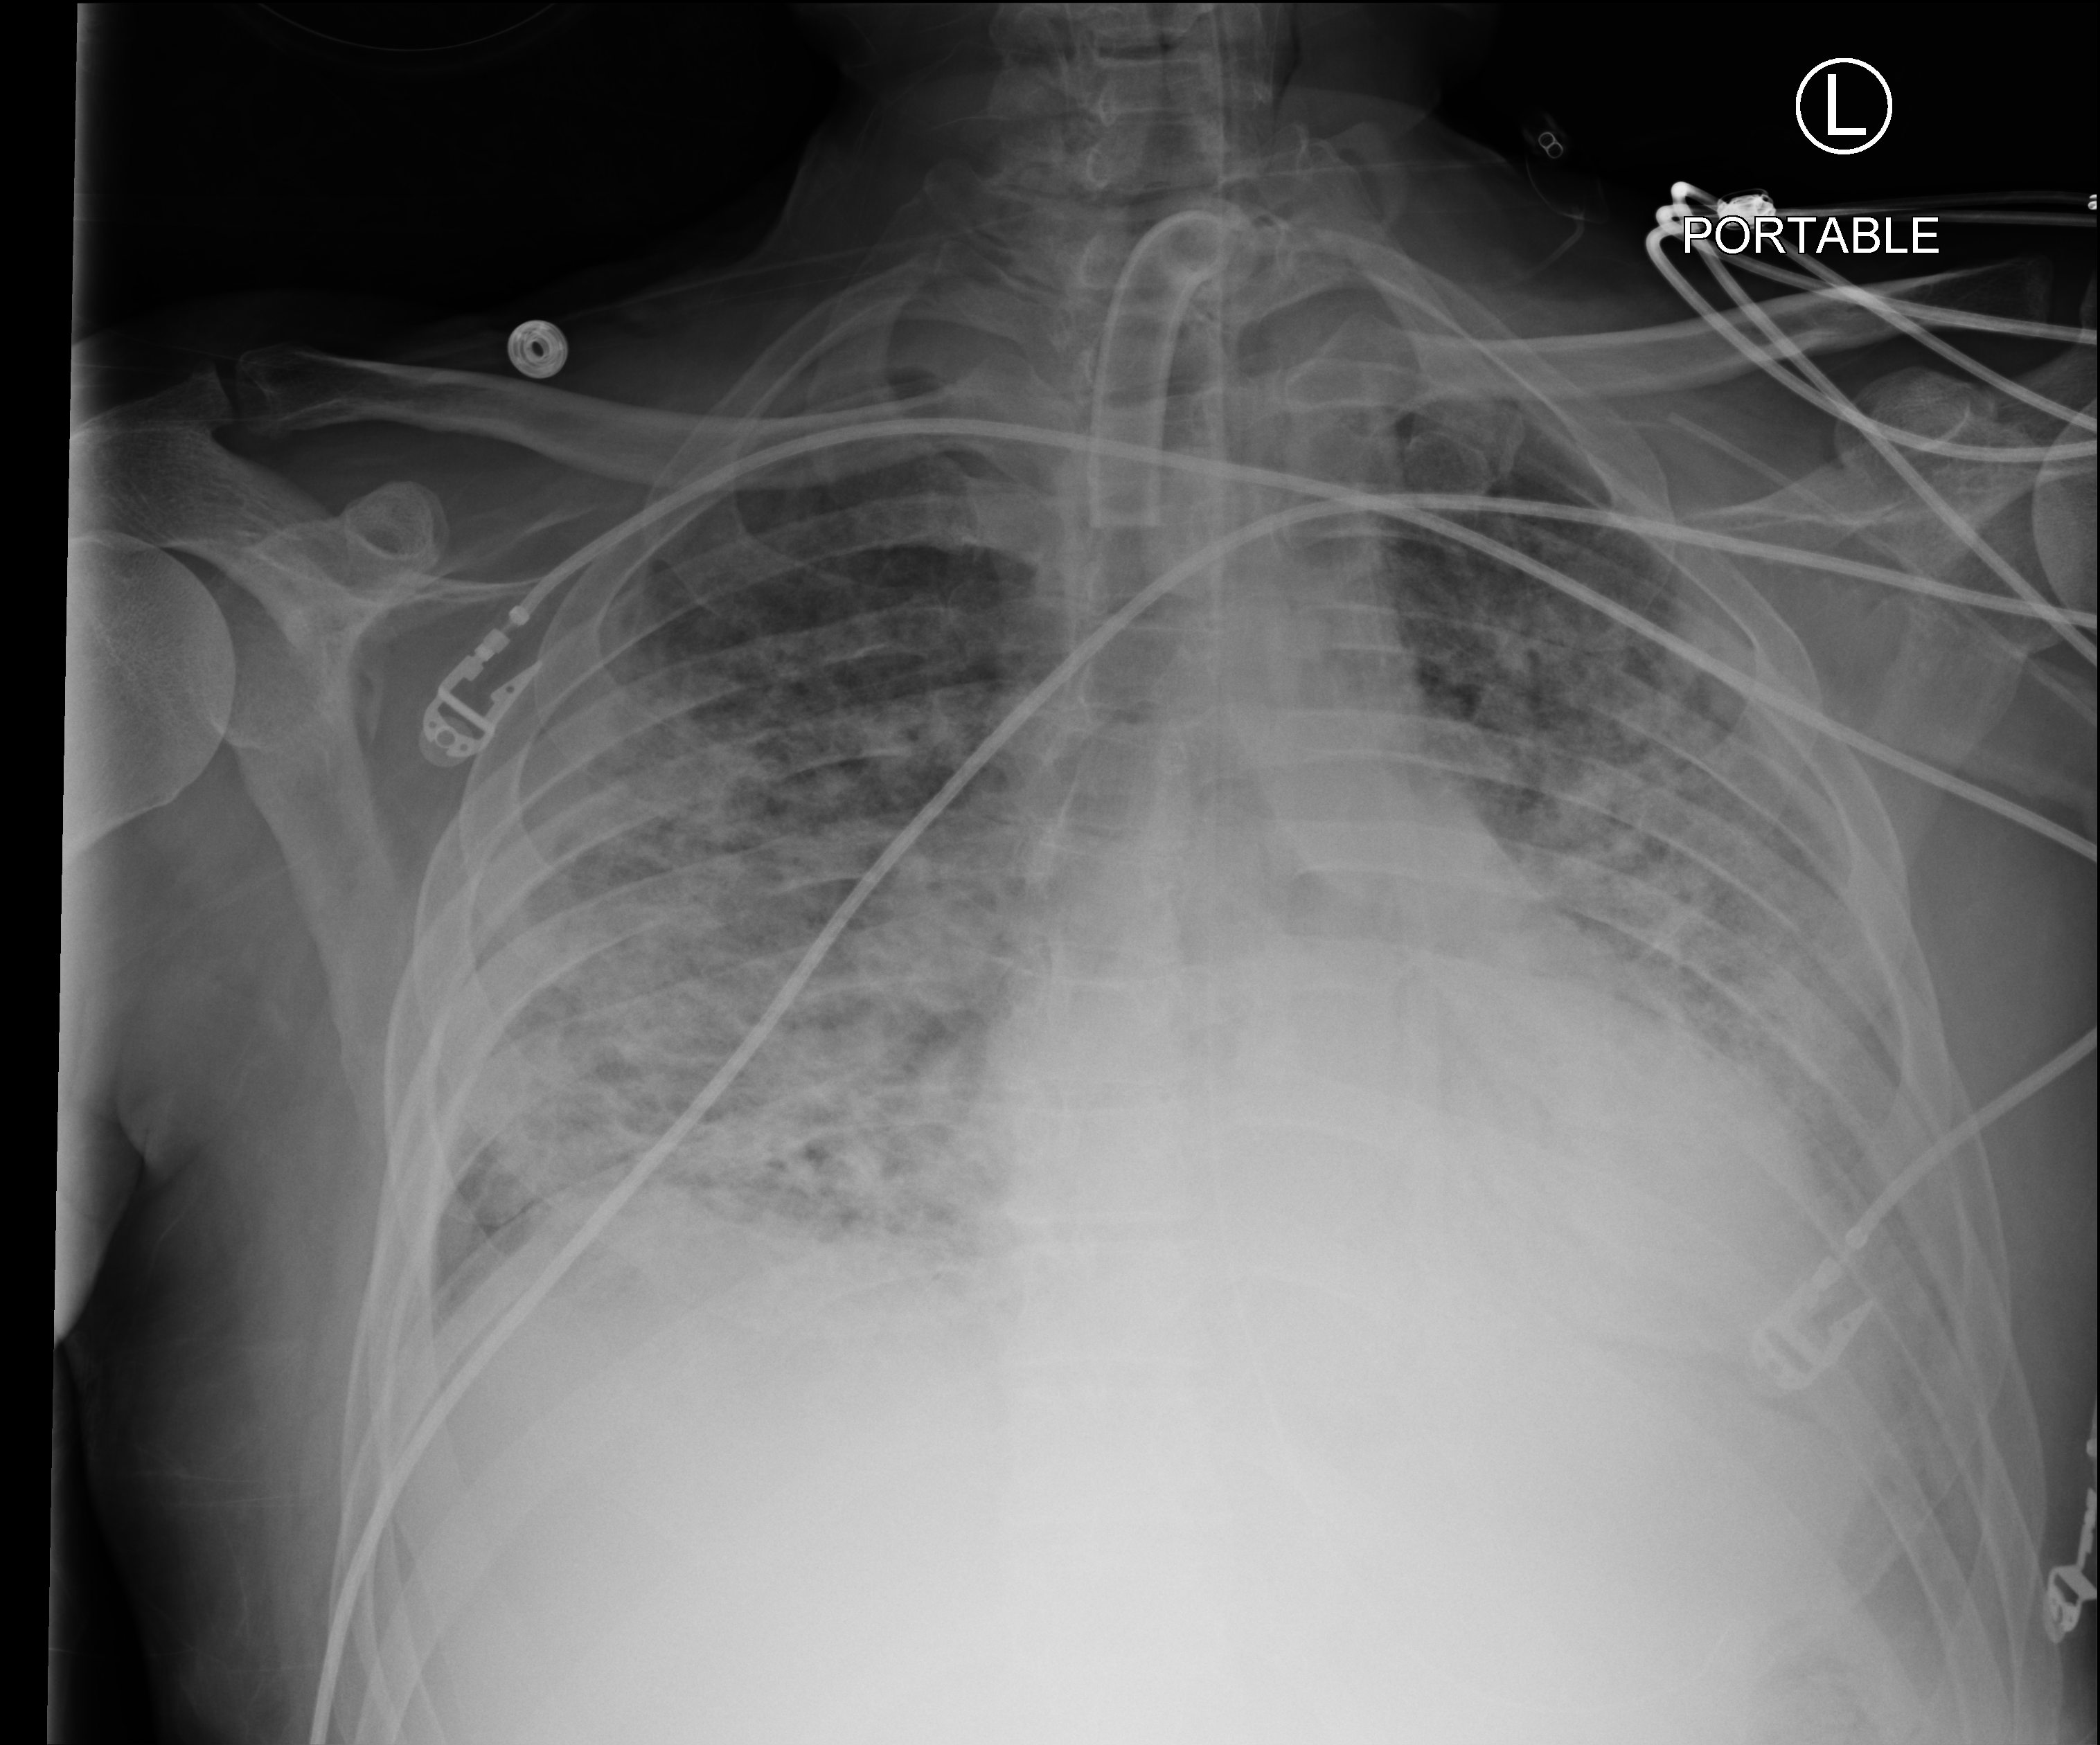
Bedside chest radiograph (computed radiography); anteroposterior (AP) projection. Male patient hospitalised with COVID-19, age 18–59 years.
Admission-level facts for this patient (not findings on this image; timing relative to this image not recorded): admitted to intensive care during this hospital stay: yes.